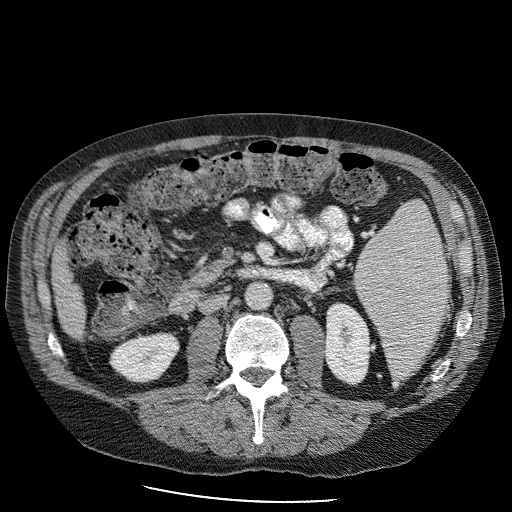
Contrast-enhanced abdominal CT (liver protocol), one axial slice. Soft-tissue window (W 400 / L 40 HU). 512 × 512 image matrix, field of view 400 × 400 mm. Case-level facts recorded for this patient, not image findings: diagnosis: hepatocellular carcinoma (patient treated with transarterial chemoembolisation; whether this scan precedes or follows treatment is not stated here); TNM stage (as recorded): Stage-II; Child-Pugh class: B; tumour differentiation: moderately differentiated; tumour nodularity: uninodular.
Structures marked on this image (semi-automatically segmented with operator editing):
- liver parenchyma outside the tumour (the mass and vessels are separate outlines, so this box may not span the whole liver): box from (x=50, y=230) to (x=86, y=339) px